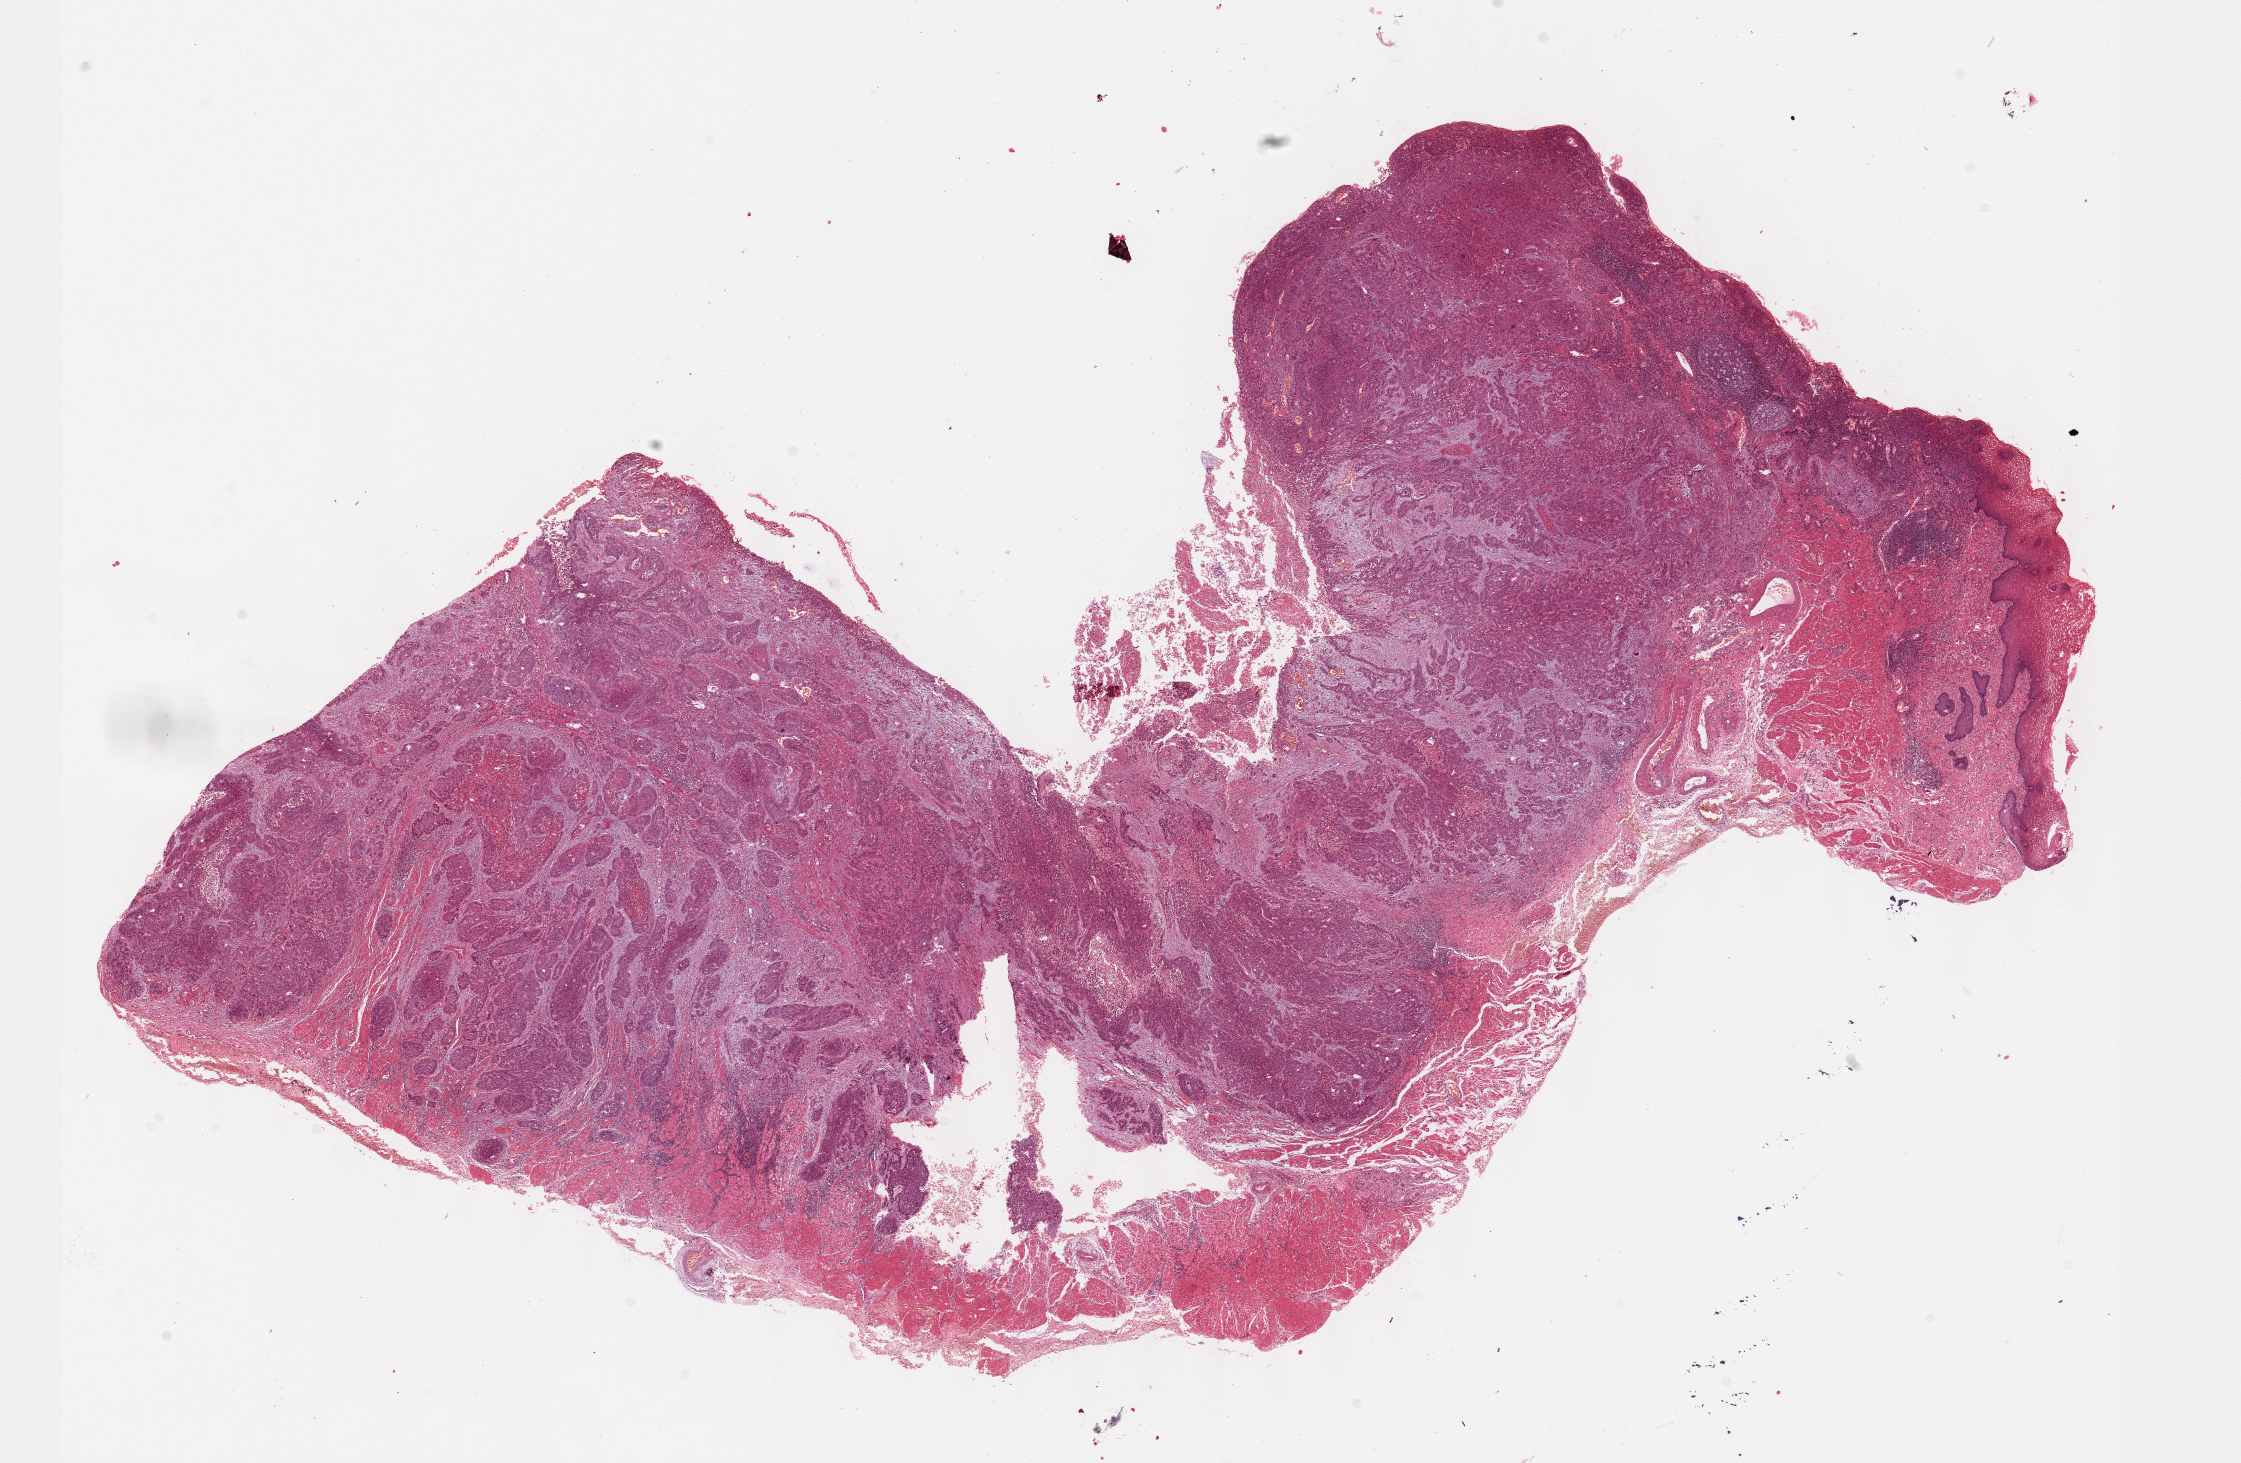
Whole-slide histology image, H&E, low-resolution overview of the scanned area, about 18.1 x 11.8 mm (slide scanned at 40x). Formalin-fixed paraffin-embedded (FFPE) diagnostic section. Sample: primary tumour, esophagus. Male, age 56 years at initial diagnosis. Histologic grade: G3 (poorly differentiated).
Histologic diagnosis: Squamous cell carcinoma, NOS (middle third of esophagus). AJCC pathologic stage: IIA.